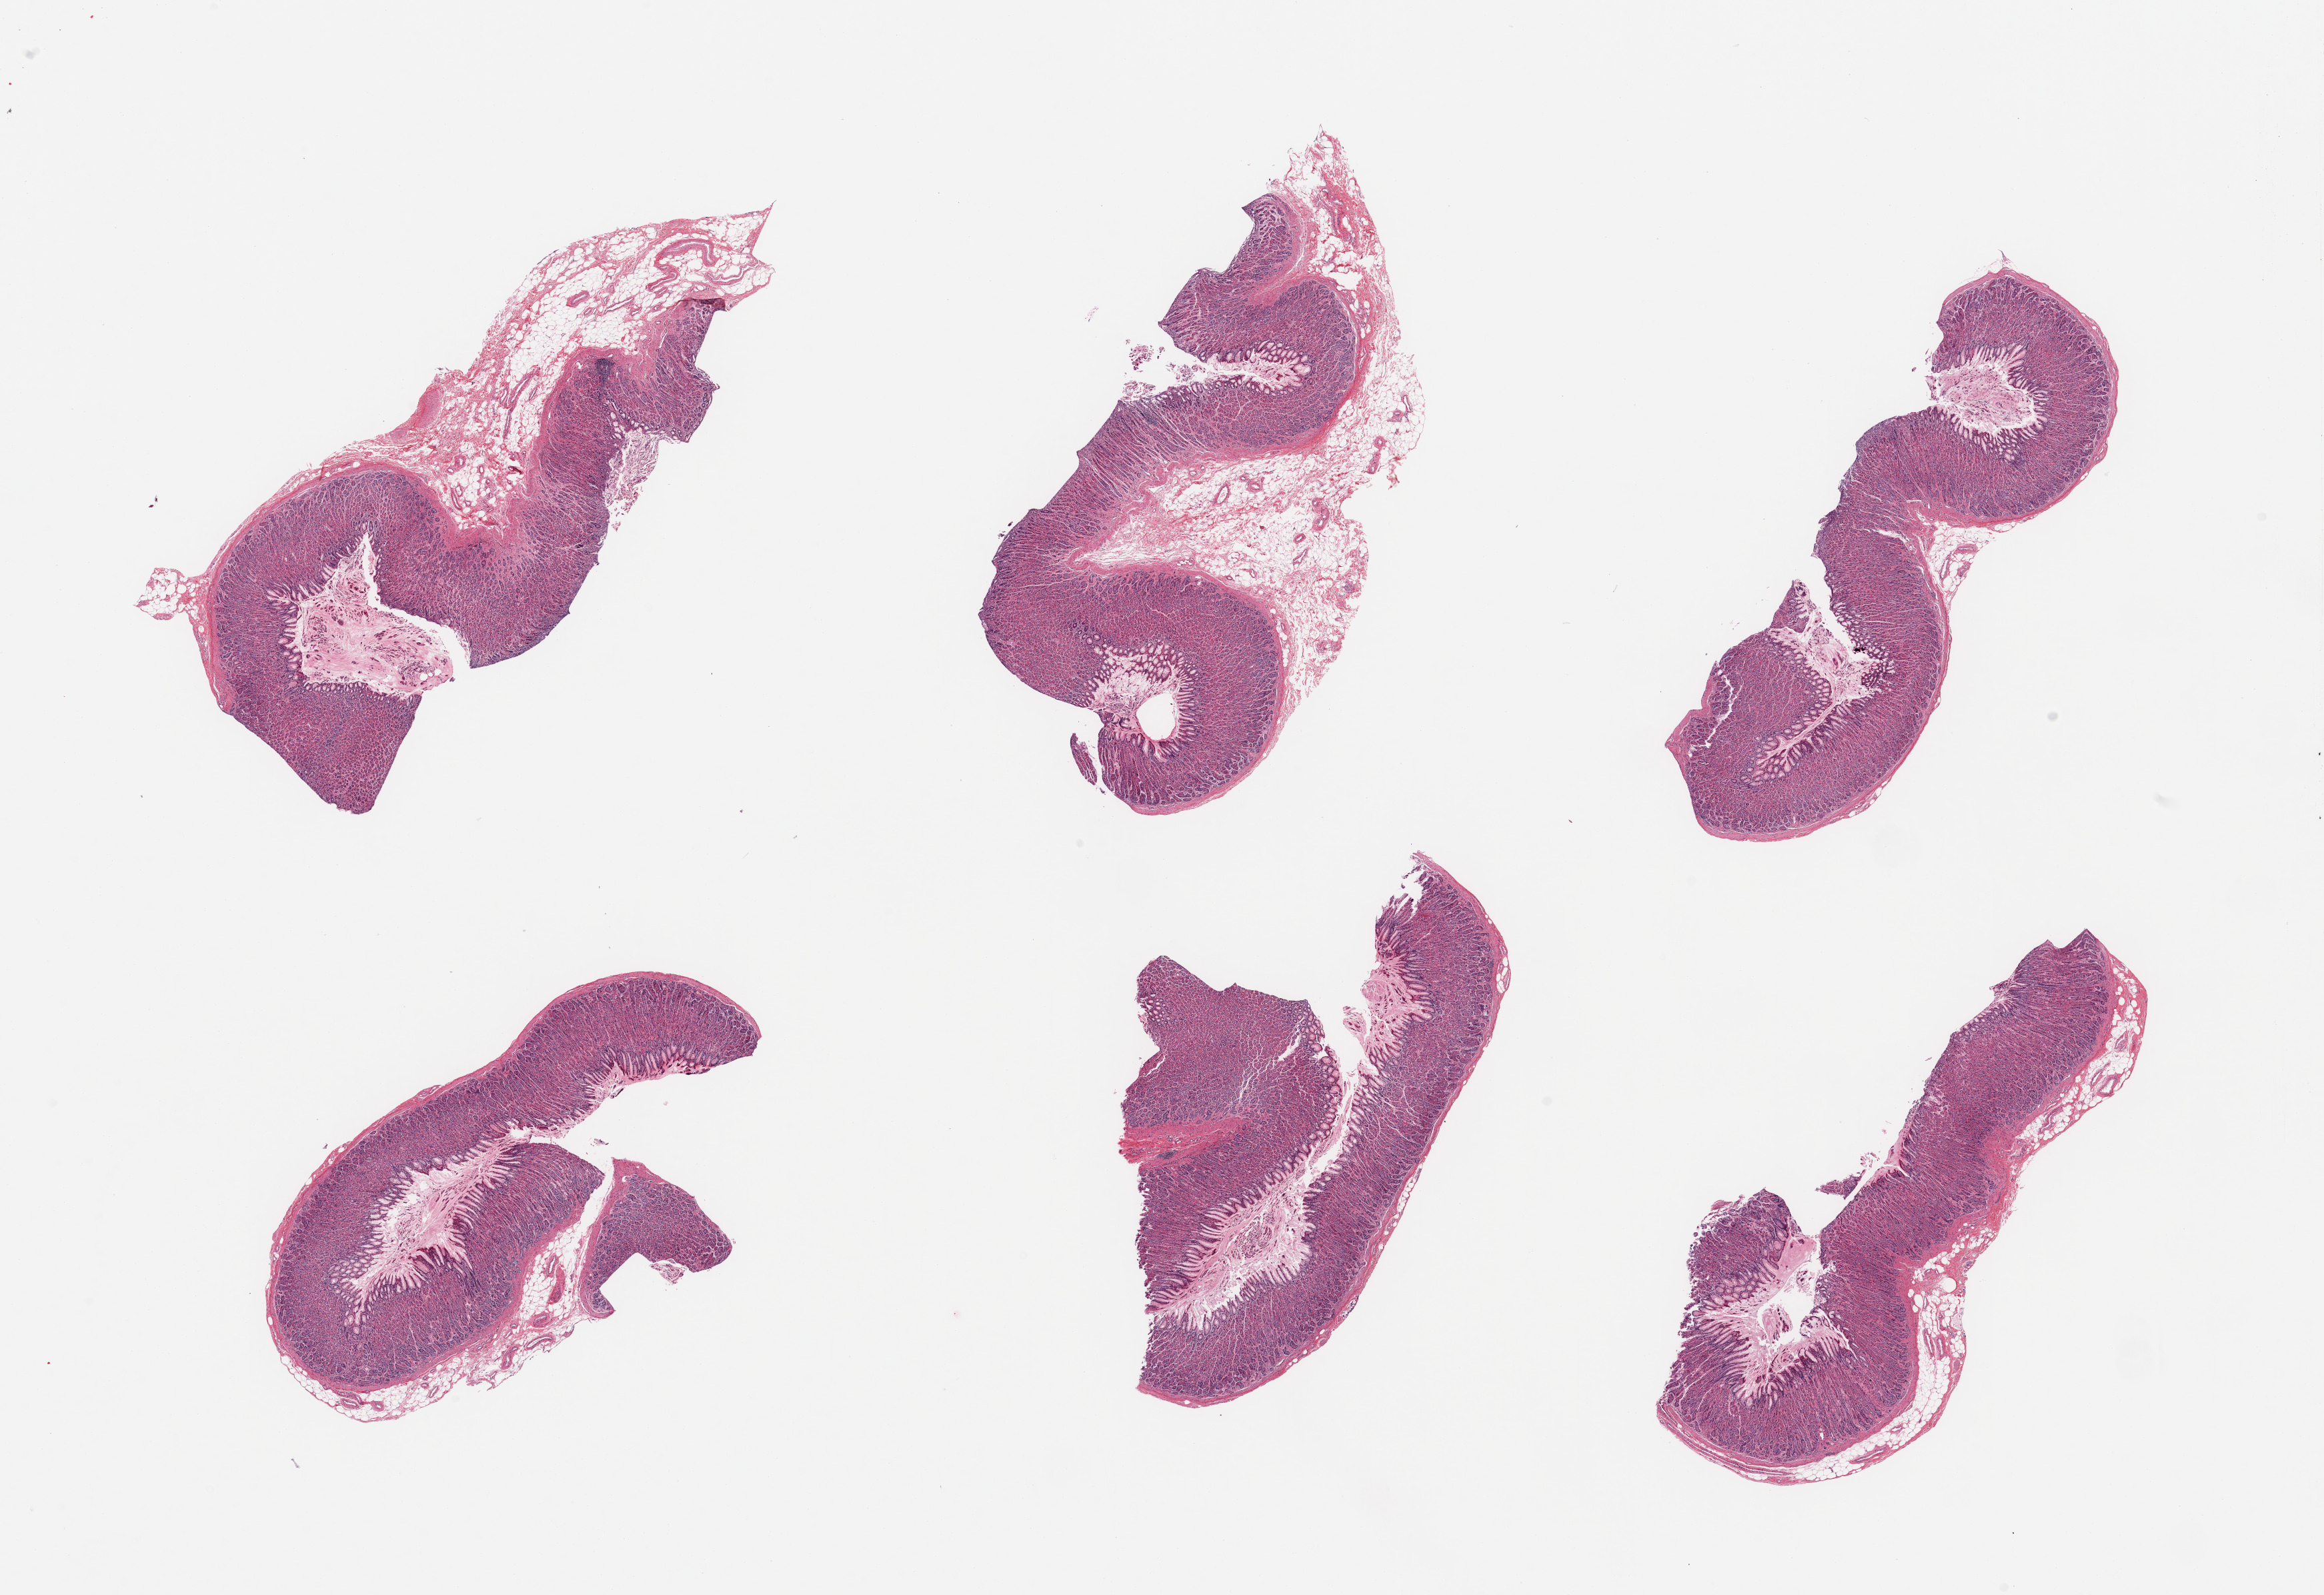
H&E whole-slide image, a low-resolution overview of the entire scanned area, about 27.6 x 18.9 mm; PAXgene-fixed paraffin-embedded (PFPE) section; sampled site (target tissue): stomach; donor tissue sample. Donor sex: female.
Reviewer comment on this tissue sample: 6 pieces; mucosa and submucosa only, no muscularis propria.